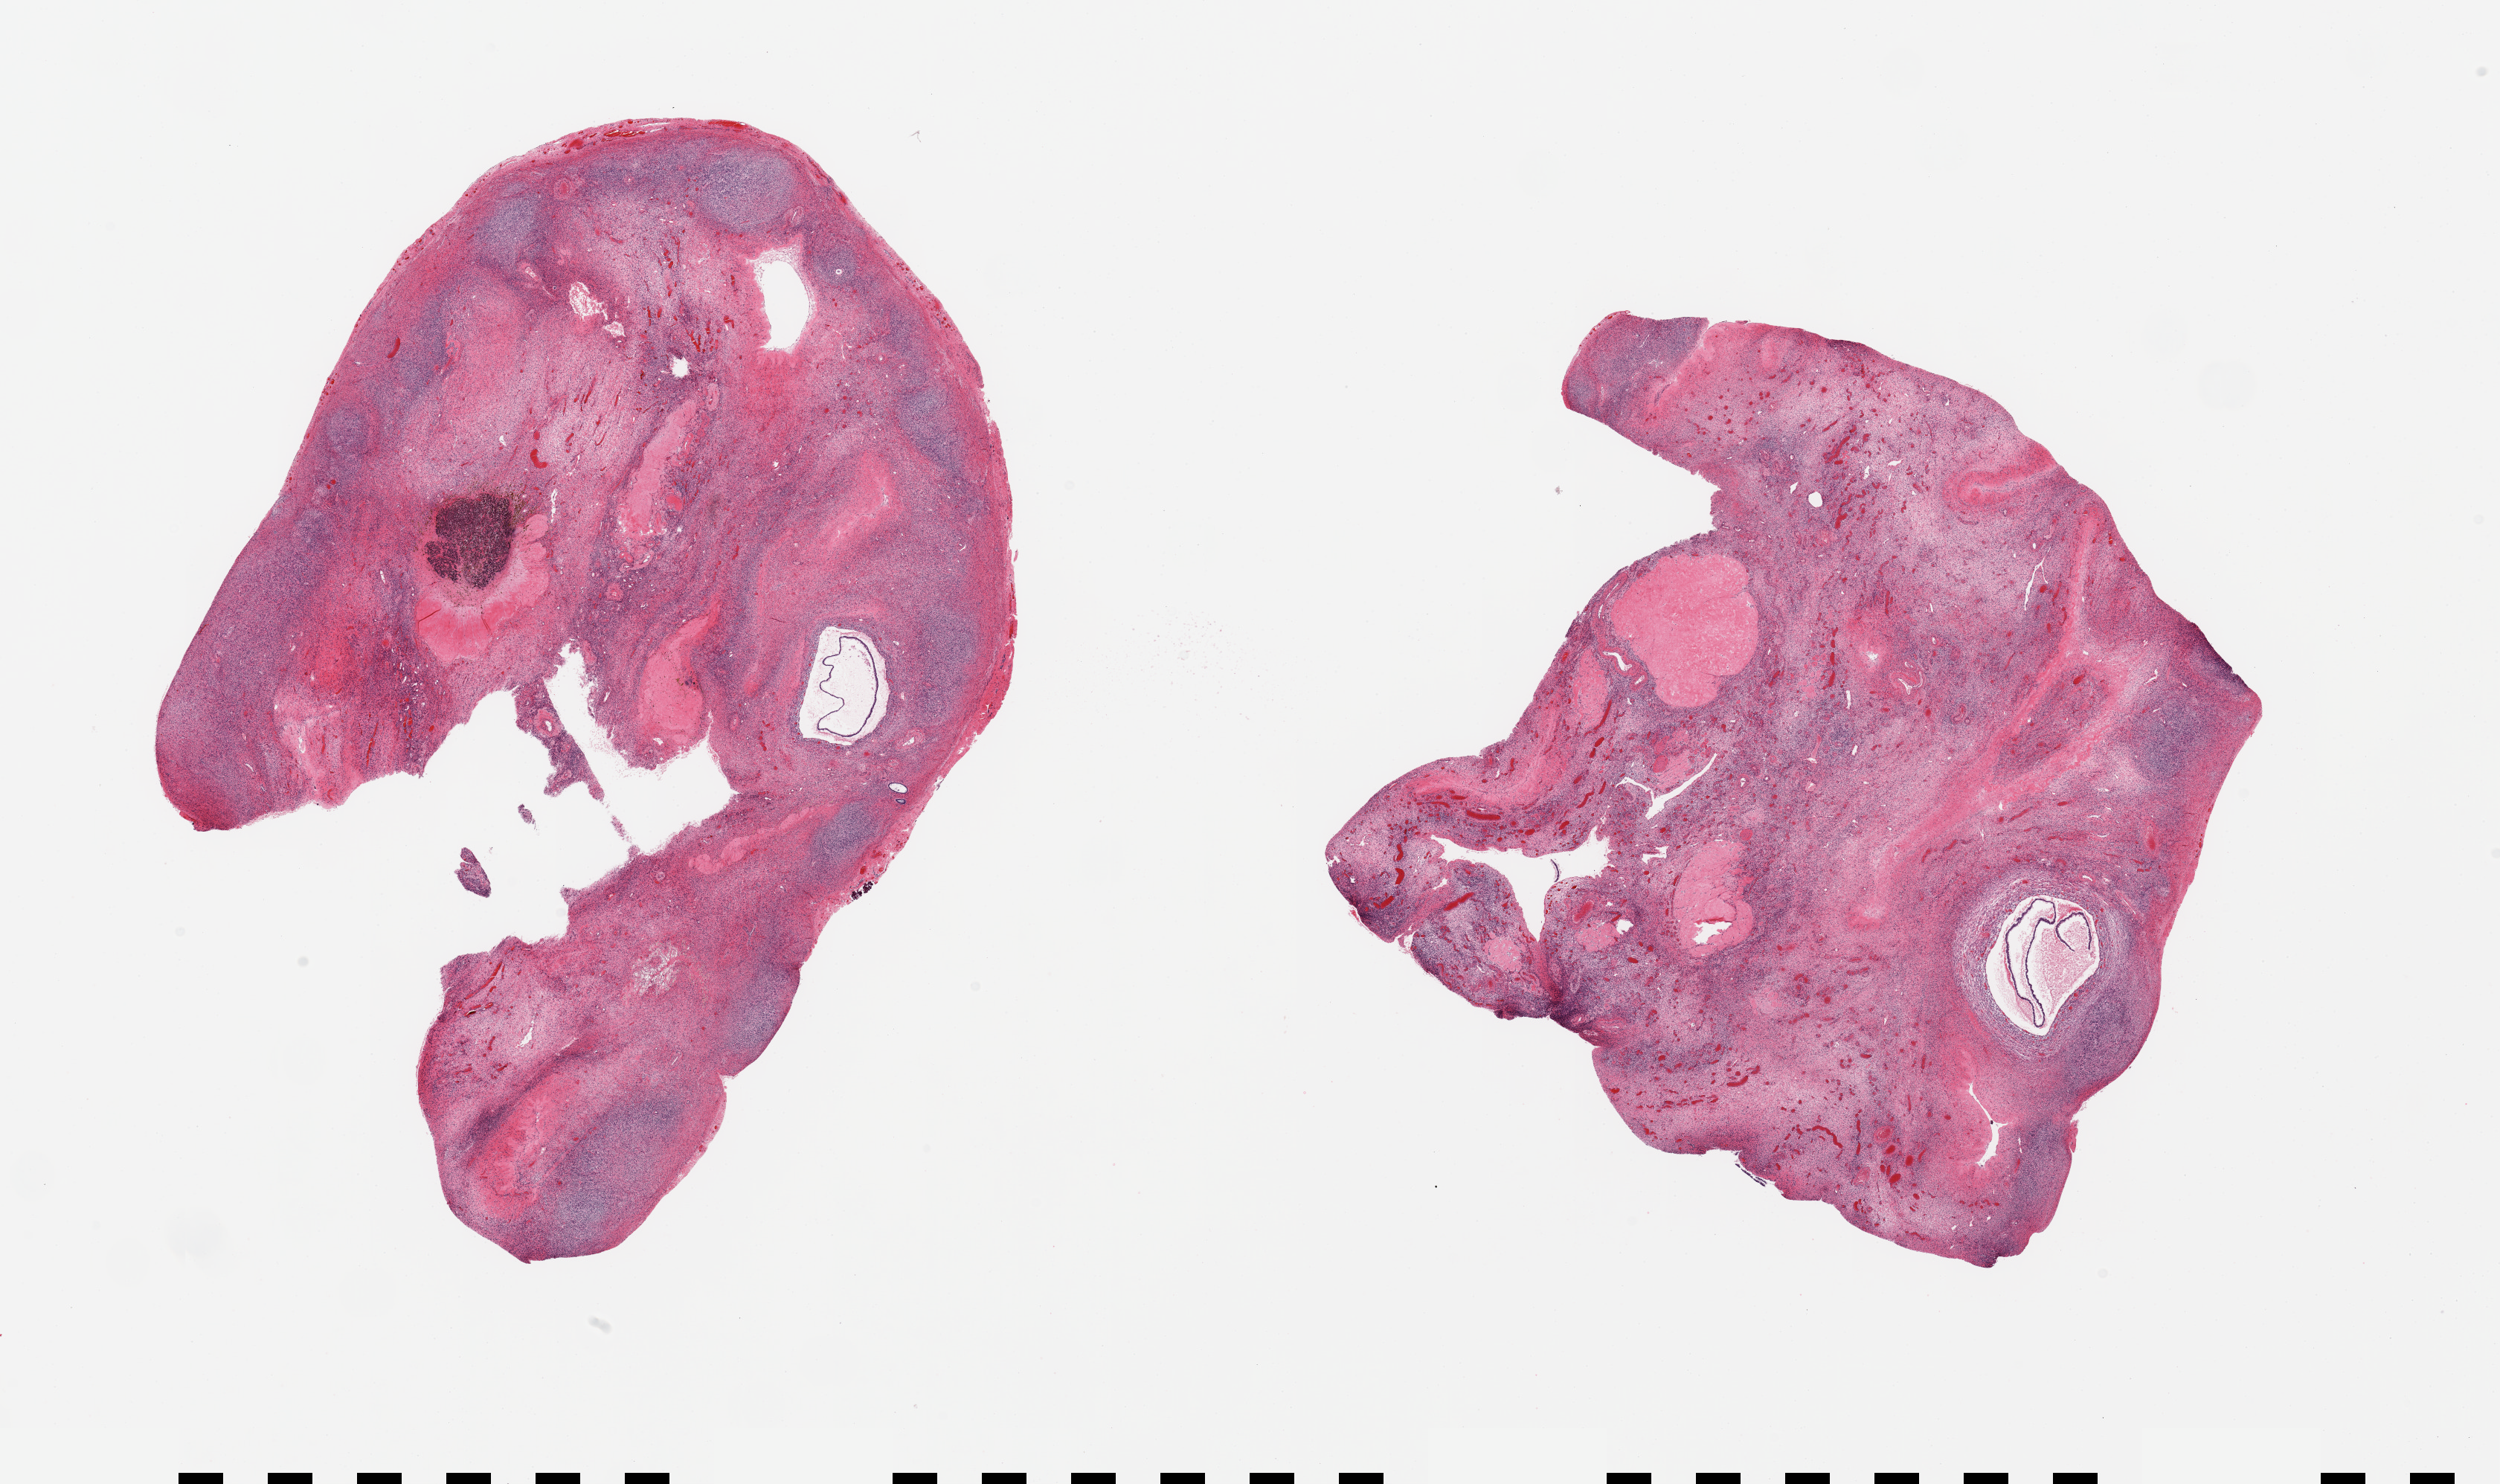
Digitized haematoxylin and eosin-stained section, brightfield, whole scanned area (about 26.6 x 15.8 mm, from a 20x scan) shown as a low-resolution overview; PAXgene-fixed paraffin-embedded (PFPE) section; sampled site (target tissue): ovary; donor tissue sample.
Pathologist's review note for this sample: 2 pieces; ova and corpora identified.